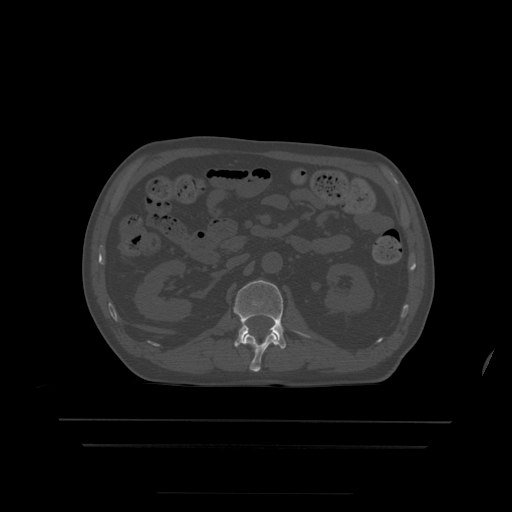
CT including the spine, one axial slice. Position 155 of 522 along the scan axis. Bone window (W 1800 / L 400 HU). 1.25 mm slice thickness. 512 × 512 image matrix. Patient age 68 years. From the clinical record (not read from this slice): primary cancer: urothelial.
Annotated regions visible in this slice (semi-automatic segmentation, software-assisted and operator-edited):
- L1 vertebra: bounding box (x1, y1, x2, y2) in pixels: (245, 333, 278, 372)
- L2 vertebra: (234, 280, 310, 349)